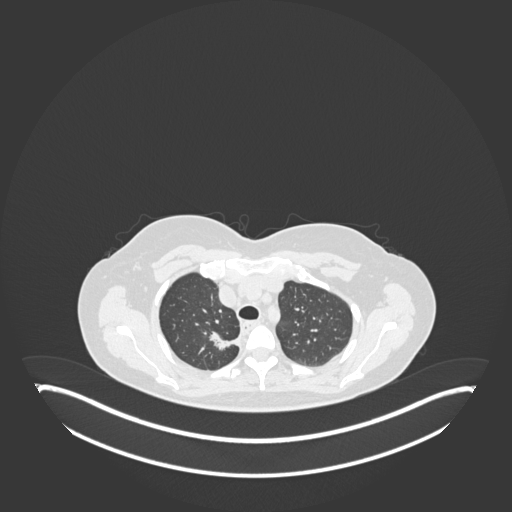
Chest CT, one axial slice; slice 141 of 181 in the series (ordered by position); reconstruction kernel B30f; lung window (W 1500 / L -600 HU); 512 × 512 image matrix, field of view 500 × 500 mm. Patient: female, 65 years. Case-level facts recorded for this patient, not image findings: clinical TNM (as recorded): T1b N0 M0; histopathological grade: G2.
Structures marked on this image (rectangle marked by the reading radiologist):
- lung tumour (recorded histology: adenocarcinoma): bounding box (x1, y1, x2, y2) in pixels: (208, 329, 241, 351)